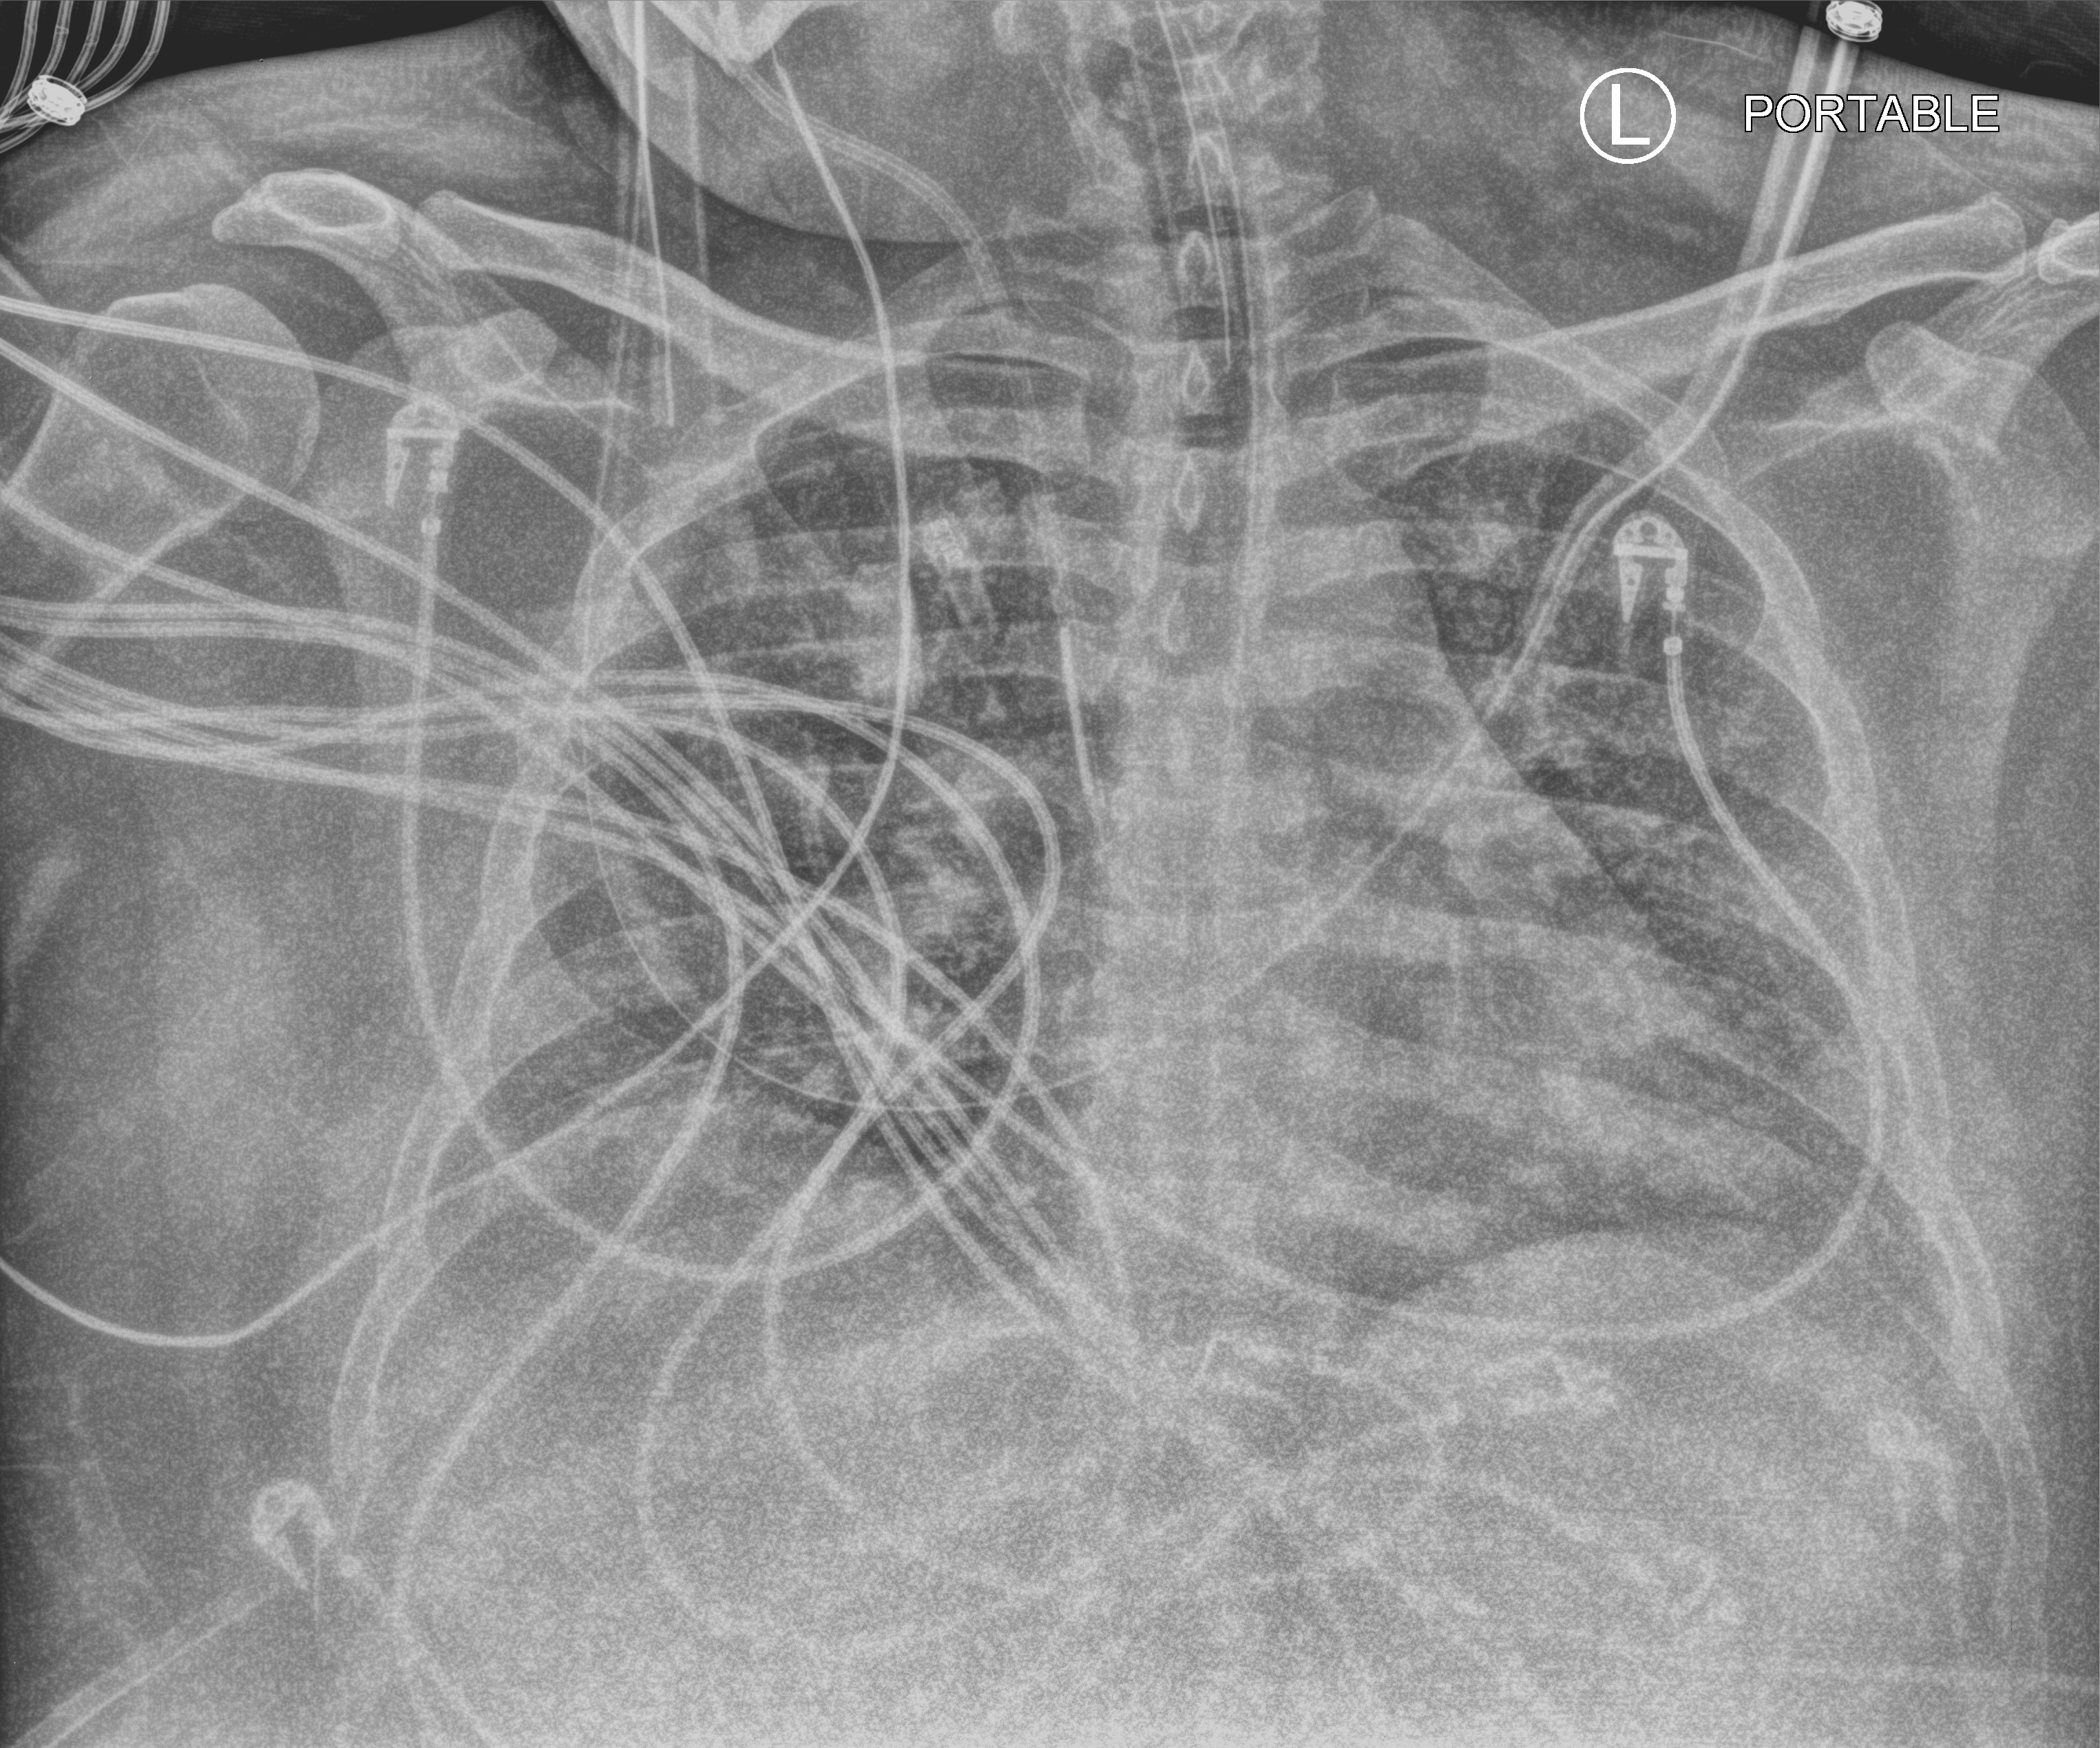
Bedside chest radiograph (computed radiography), anteroposterior (AP) projection. Patient hospitalised with COVID-19, aged 18–59 years.
From the hospital-stay record, not from the radiograph (when in the stay this image was taken is not recorded): admitted to intensive care during this hospital stay: yes; diabetes (admission record): no.